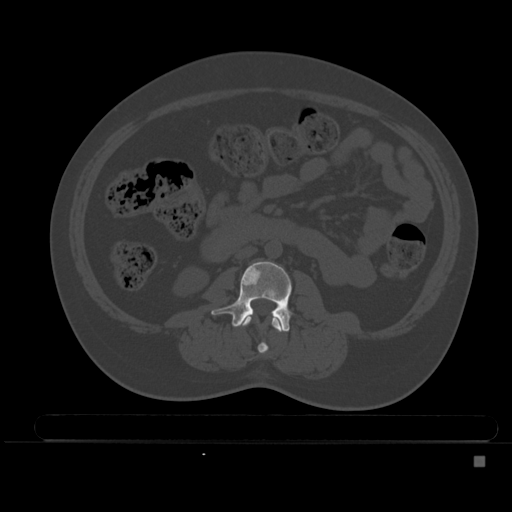
CT including the spine, one axial slice; position 157 of 495 along the scan axis; bone window (W 1800 / L 400 HU); 512 × 512 image matrix, field of view 404 × 404 mm. Patient: female, 33 years. Case-level facts recorded for this patient, not image findings: primary cancer: breast.
Structures marked on this image (semi-automatic segmentation, software-assisted and operator-edited):
- L2 vertebra: bounding box <241,314,283,354> (left, top, right, bottom; pixels)
- L3 vertebra: <211,261,292,332>